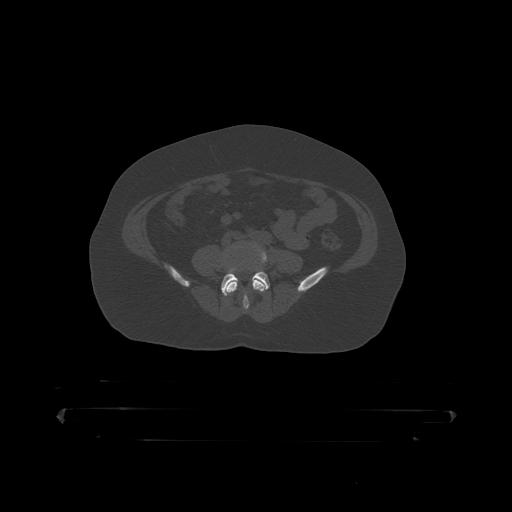
CT including the spine, one axial slice. Slice 51 of 390 in the series (ordered by position). 120 kVp. Bone window (W 1800 / L 400 HU). 1.25 mm slice thickness. 512 × 512 image matrix. Male patient, age 60 years. Case-level facts recorded for this patient, not image findings: primary cancer: prostate.
Annotated regions visible in this slice (semi-automatic segmentation, software-assisted and operator-edited):
- L4 vertebra: box from (x=222, y=242) to (x=267, y=311) px
- L5 vertebra: (x=221, y=269)–(x=270, y=296)